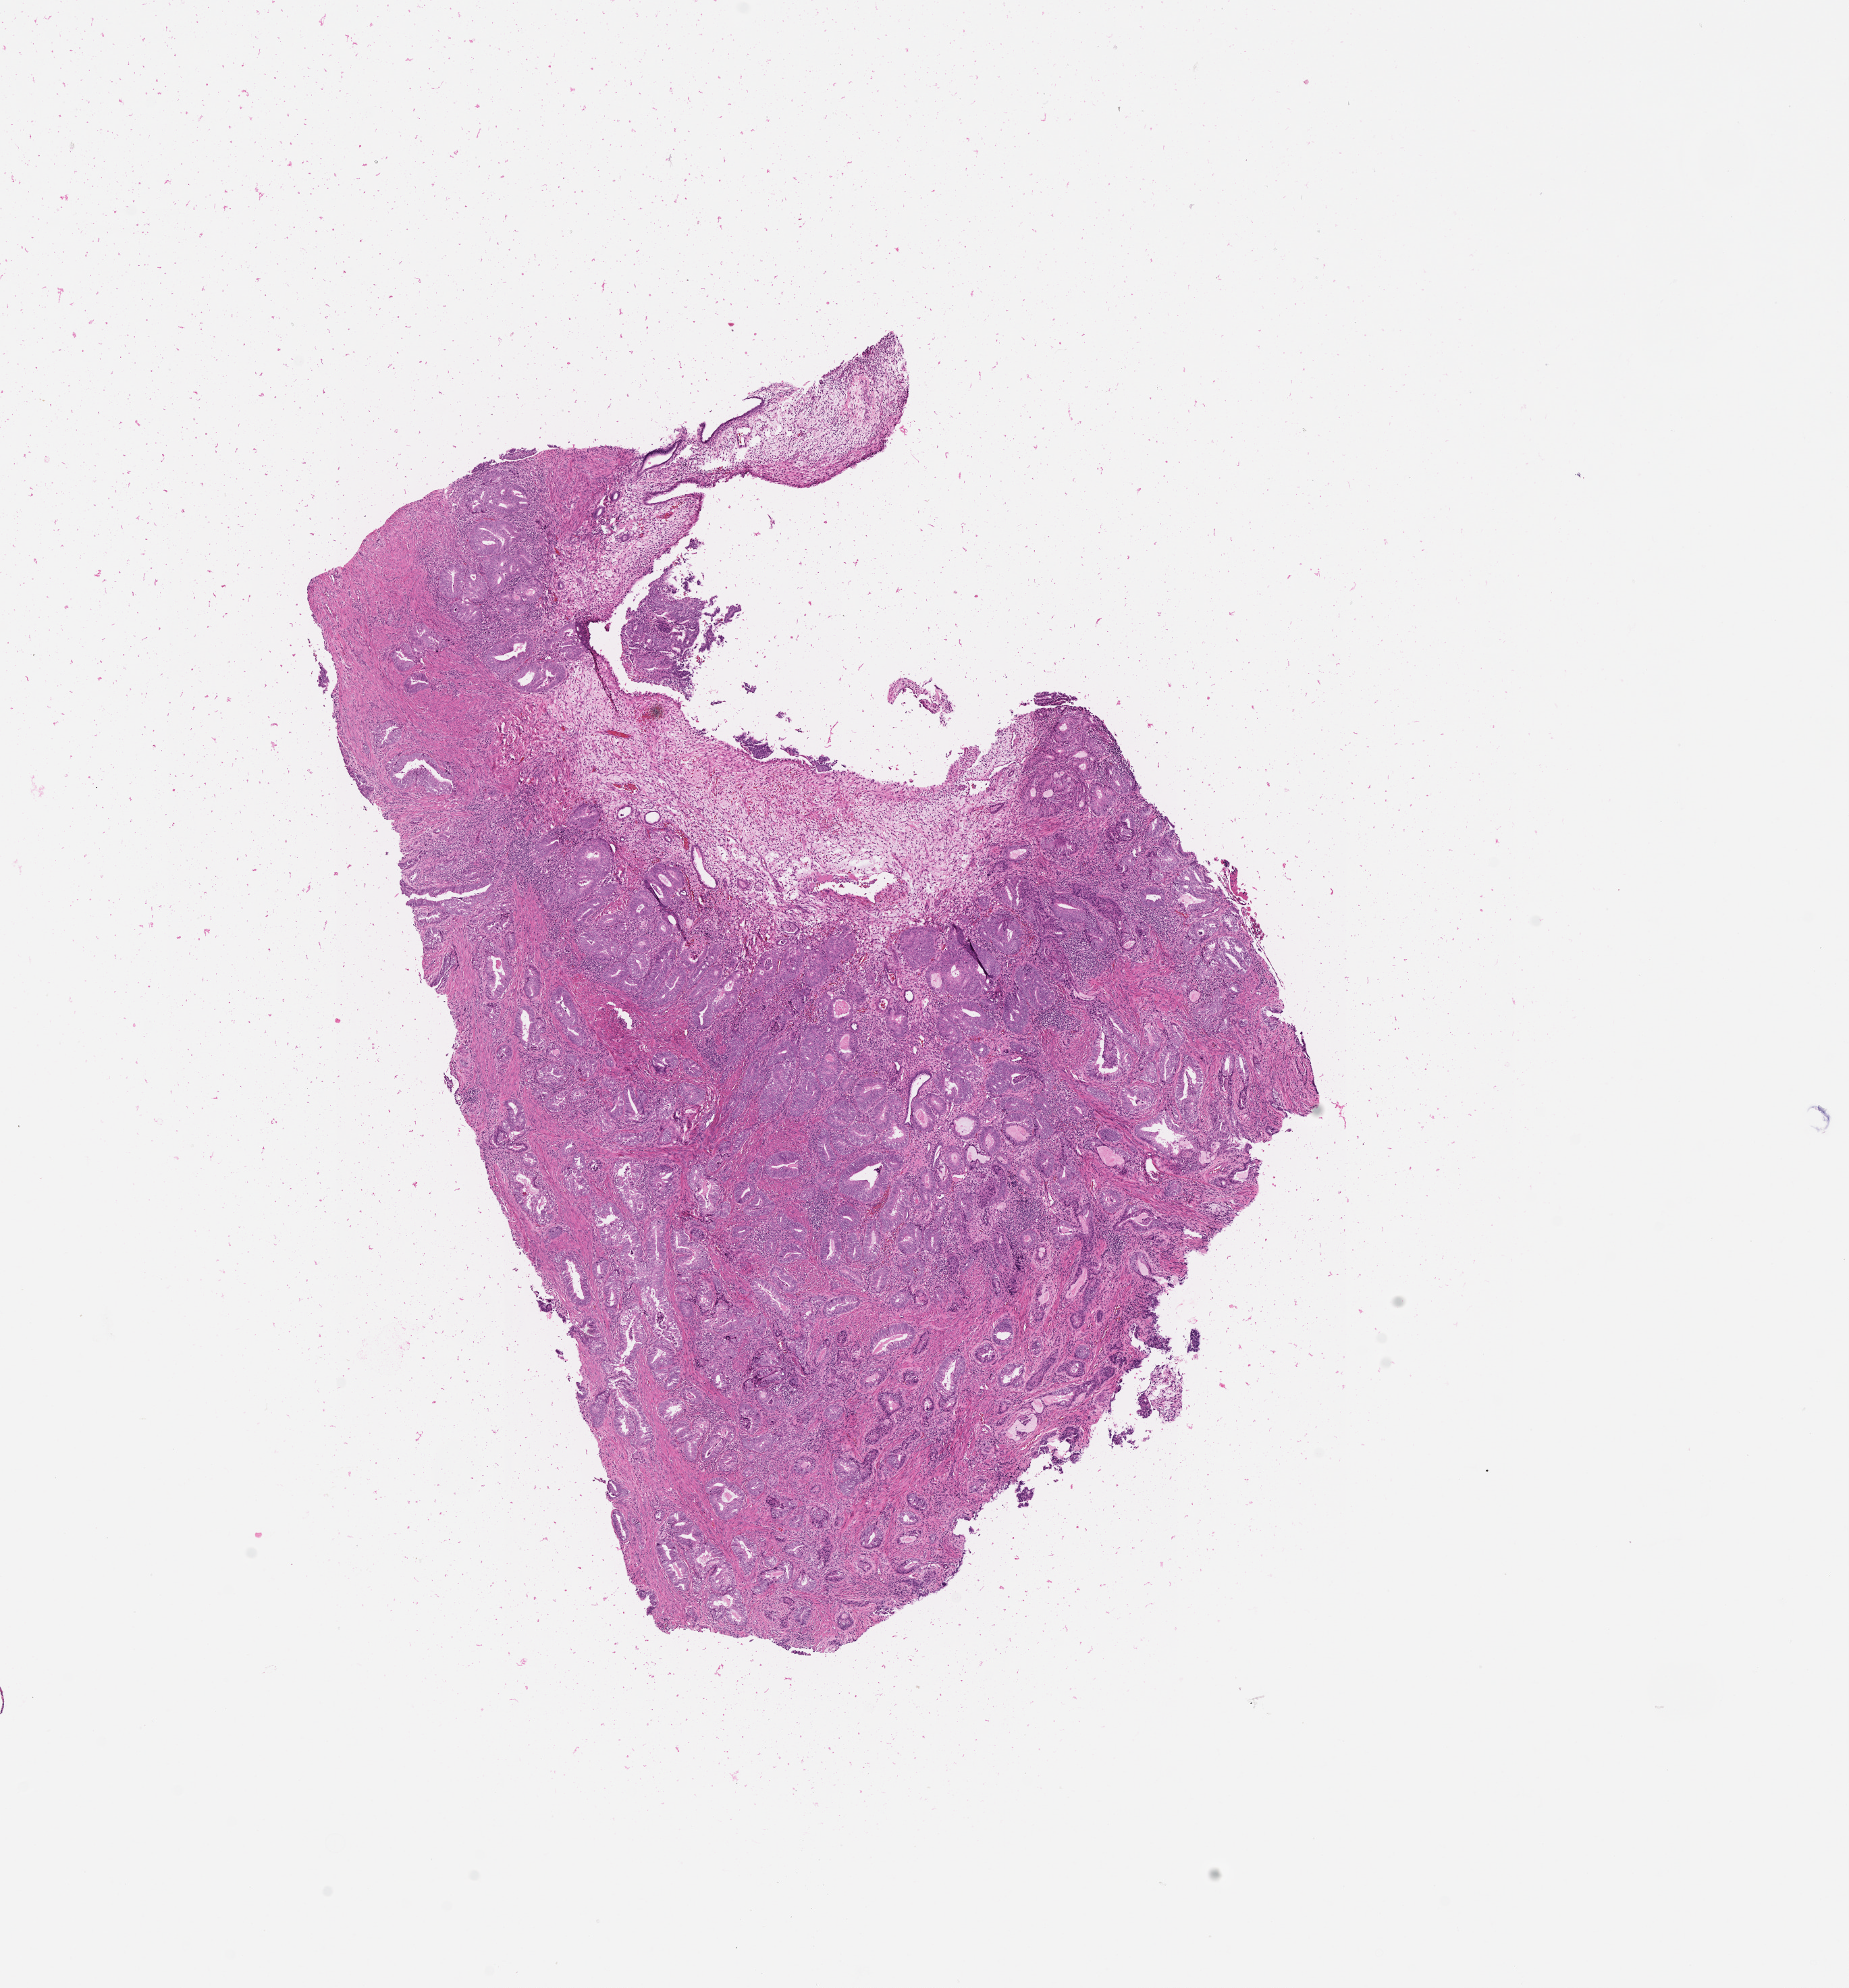
Whole-slide histology image, H&E — low-resolution overview of the scanned area, about 11.0 x 11.9 mm (acquisition: 20x scan), normal (non-tumour) tissue sample, uterus. 68-year-old female patient.
• this section: normal (non-tumour) tissue from the same patient
• patient diagnosis: Endometrioid adenocarcinoma, NOS